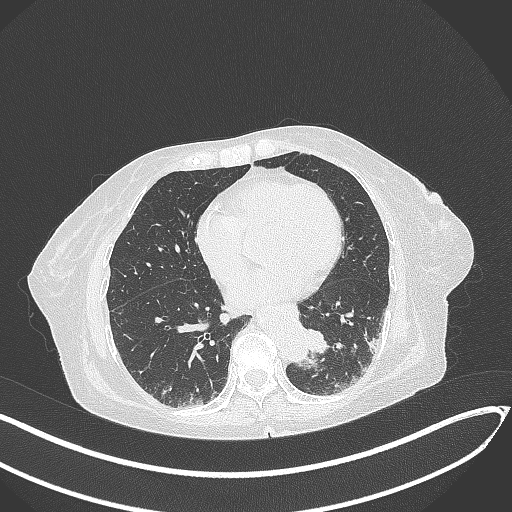
Chest CT, one axial slice. Position 84 of 324 along the scan axis. Reconstruction kernel B70f. 120 kVp. Lung window (W 1500 / L -600 HU). 512 × 512 image matrix, field of view 400 × 400 mm. Patient: female, 82 years. From the clinical record (not read from this slice): clinical TNM (as recorded): T1b N0 M1.
Structures marked on this image (bounding box drawn by a radiologist):
- lung tumour (recorded histology: adenocarcinoma): bounding box [x1, y1, x2, y2] px = [301, 325, 334, 359]